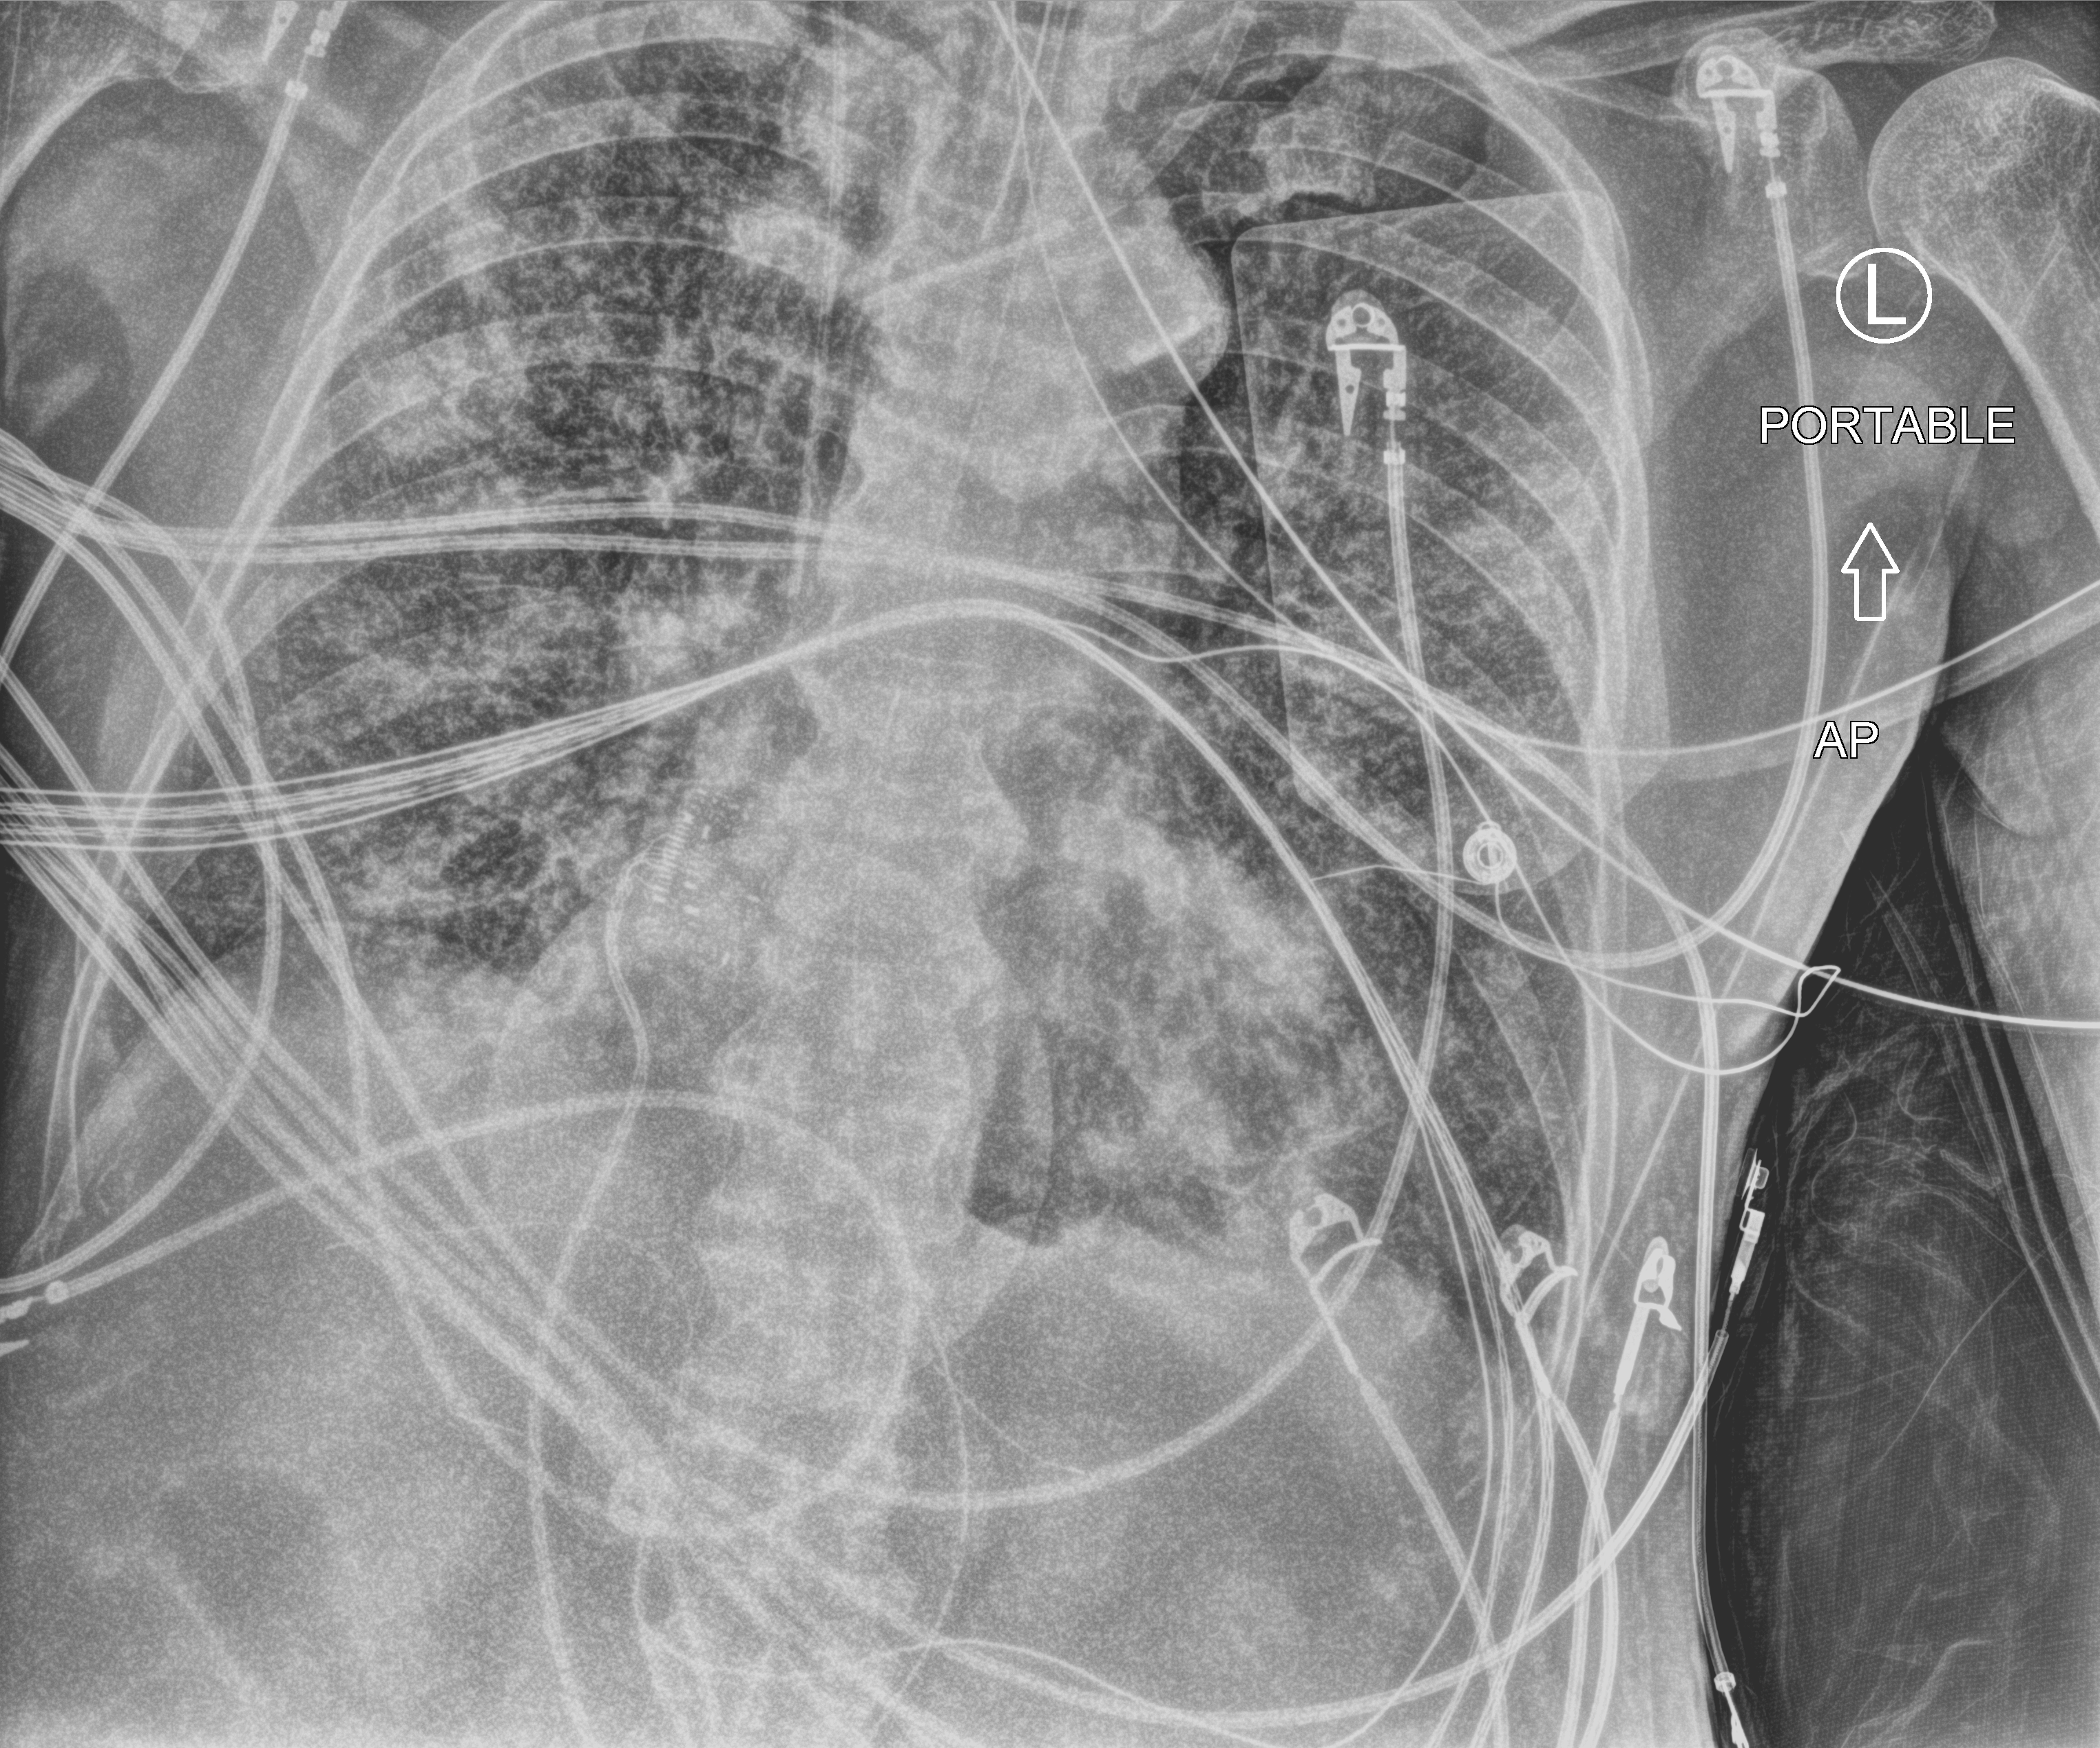
Bedside chest radiograph (computed radiography); anteroposterior (AP) projection. Male patient hospitalised with COVID-19, age 60–74 years.
From the hospital-stay record, not from the radiograph (when in the stay this image was taken is not recorded): mechanically ventilated during this hospital stay: yes; admitted to intensive care during this hospital stay: yes.